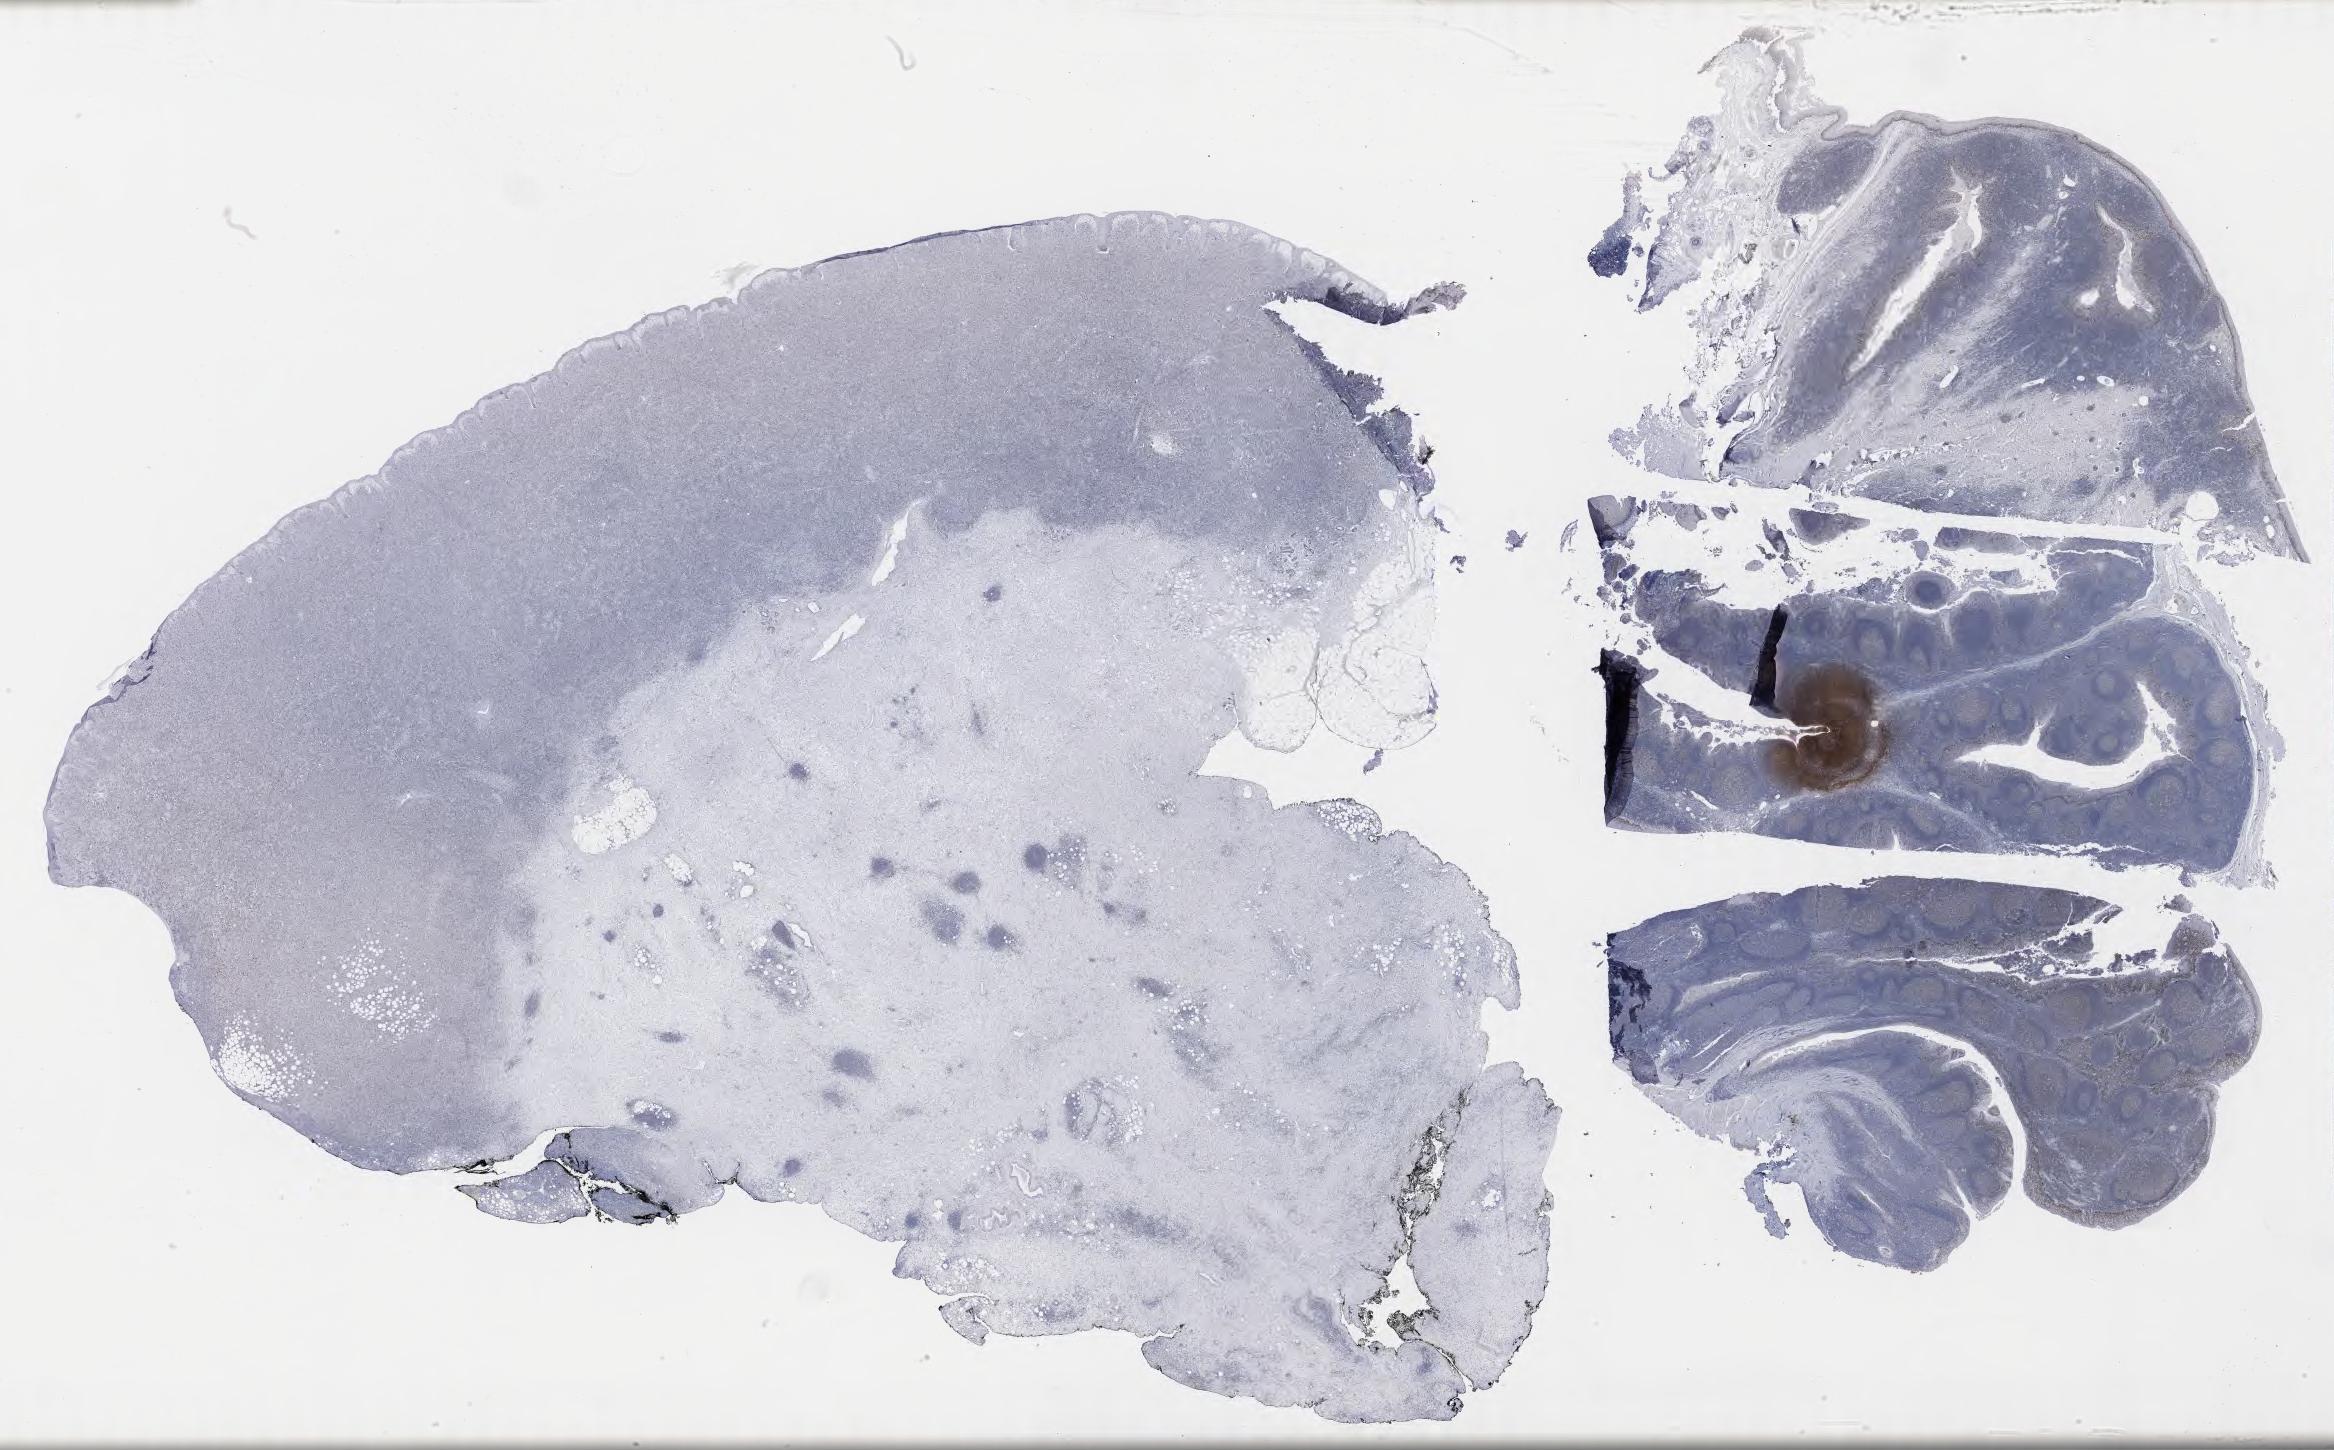
Immunohistochemistry (IHC) whole-slide image stained for p53, shown as a low-resolution overview of the whole scanned area (about 37.7 x 23.4 mm), specimen: tumor tissue, site: lymph node. Patient male; aged 52.
- histologic diagnosis: Diffuse large B-cell lymphoma, NOS